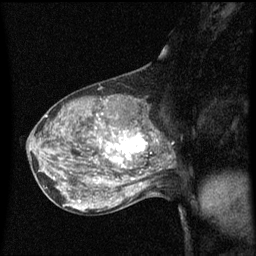
Breast MRI (dynamic contrast-enhanced), one sagittal slice. Position 33 of 60 along the scan axis. Dynamic contrast-enhanced series, image 2 of 3 at this slice position (ordered by acquisition). 1.5 T. TE 4.2 ms, TR 8.4 ms. 256 × 256 image matrix. Patient: female, 50 years.
Structures marked on this image (semi-automatically segmented with operator editing):
- analysis volume of interest (the breast-tissue region the enhancement analysis was run in; not a lesion): bounding box [x1, y1, x2, y2] px = [100, 114, 153, 171]
- tumour enhancement mask (voxels above the 70 % enhancement threshold inside the analysis volume of interest): [100, 132, 148, 163]